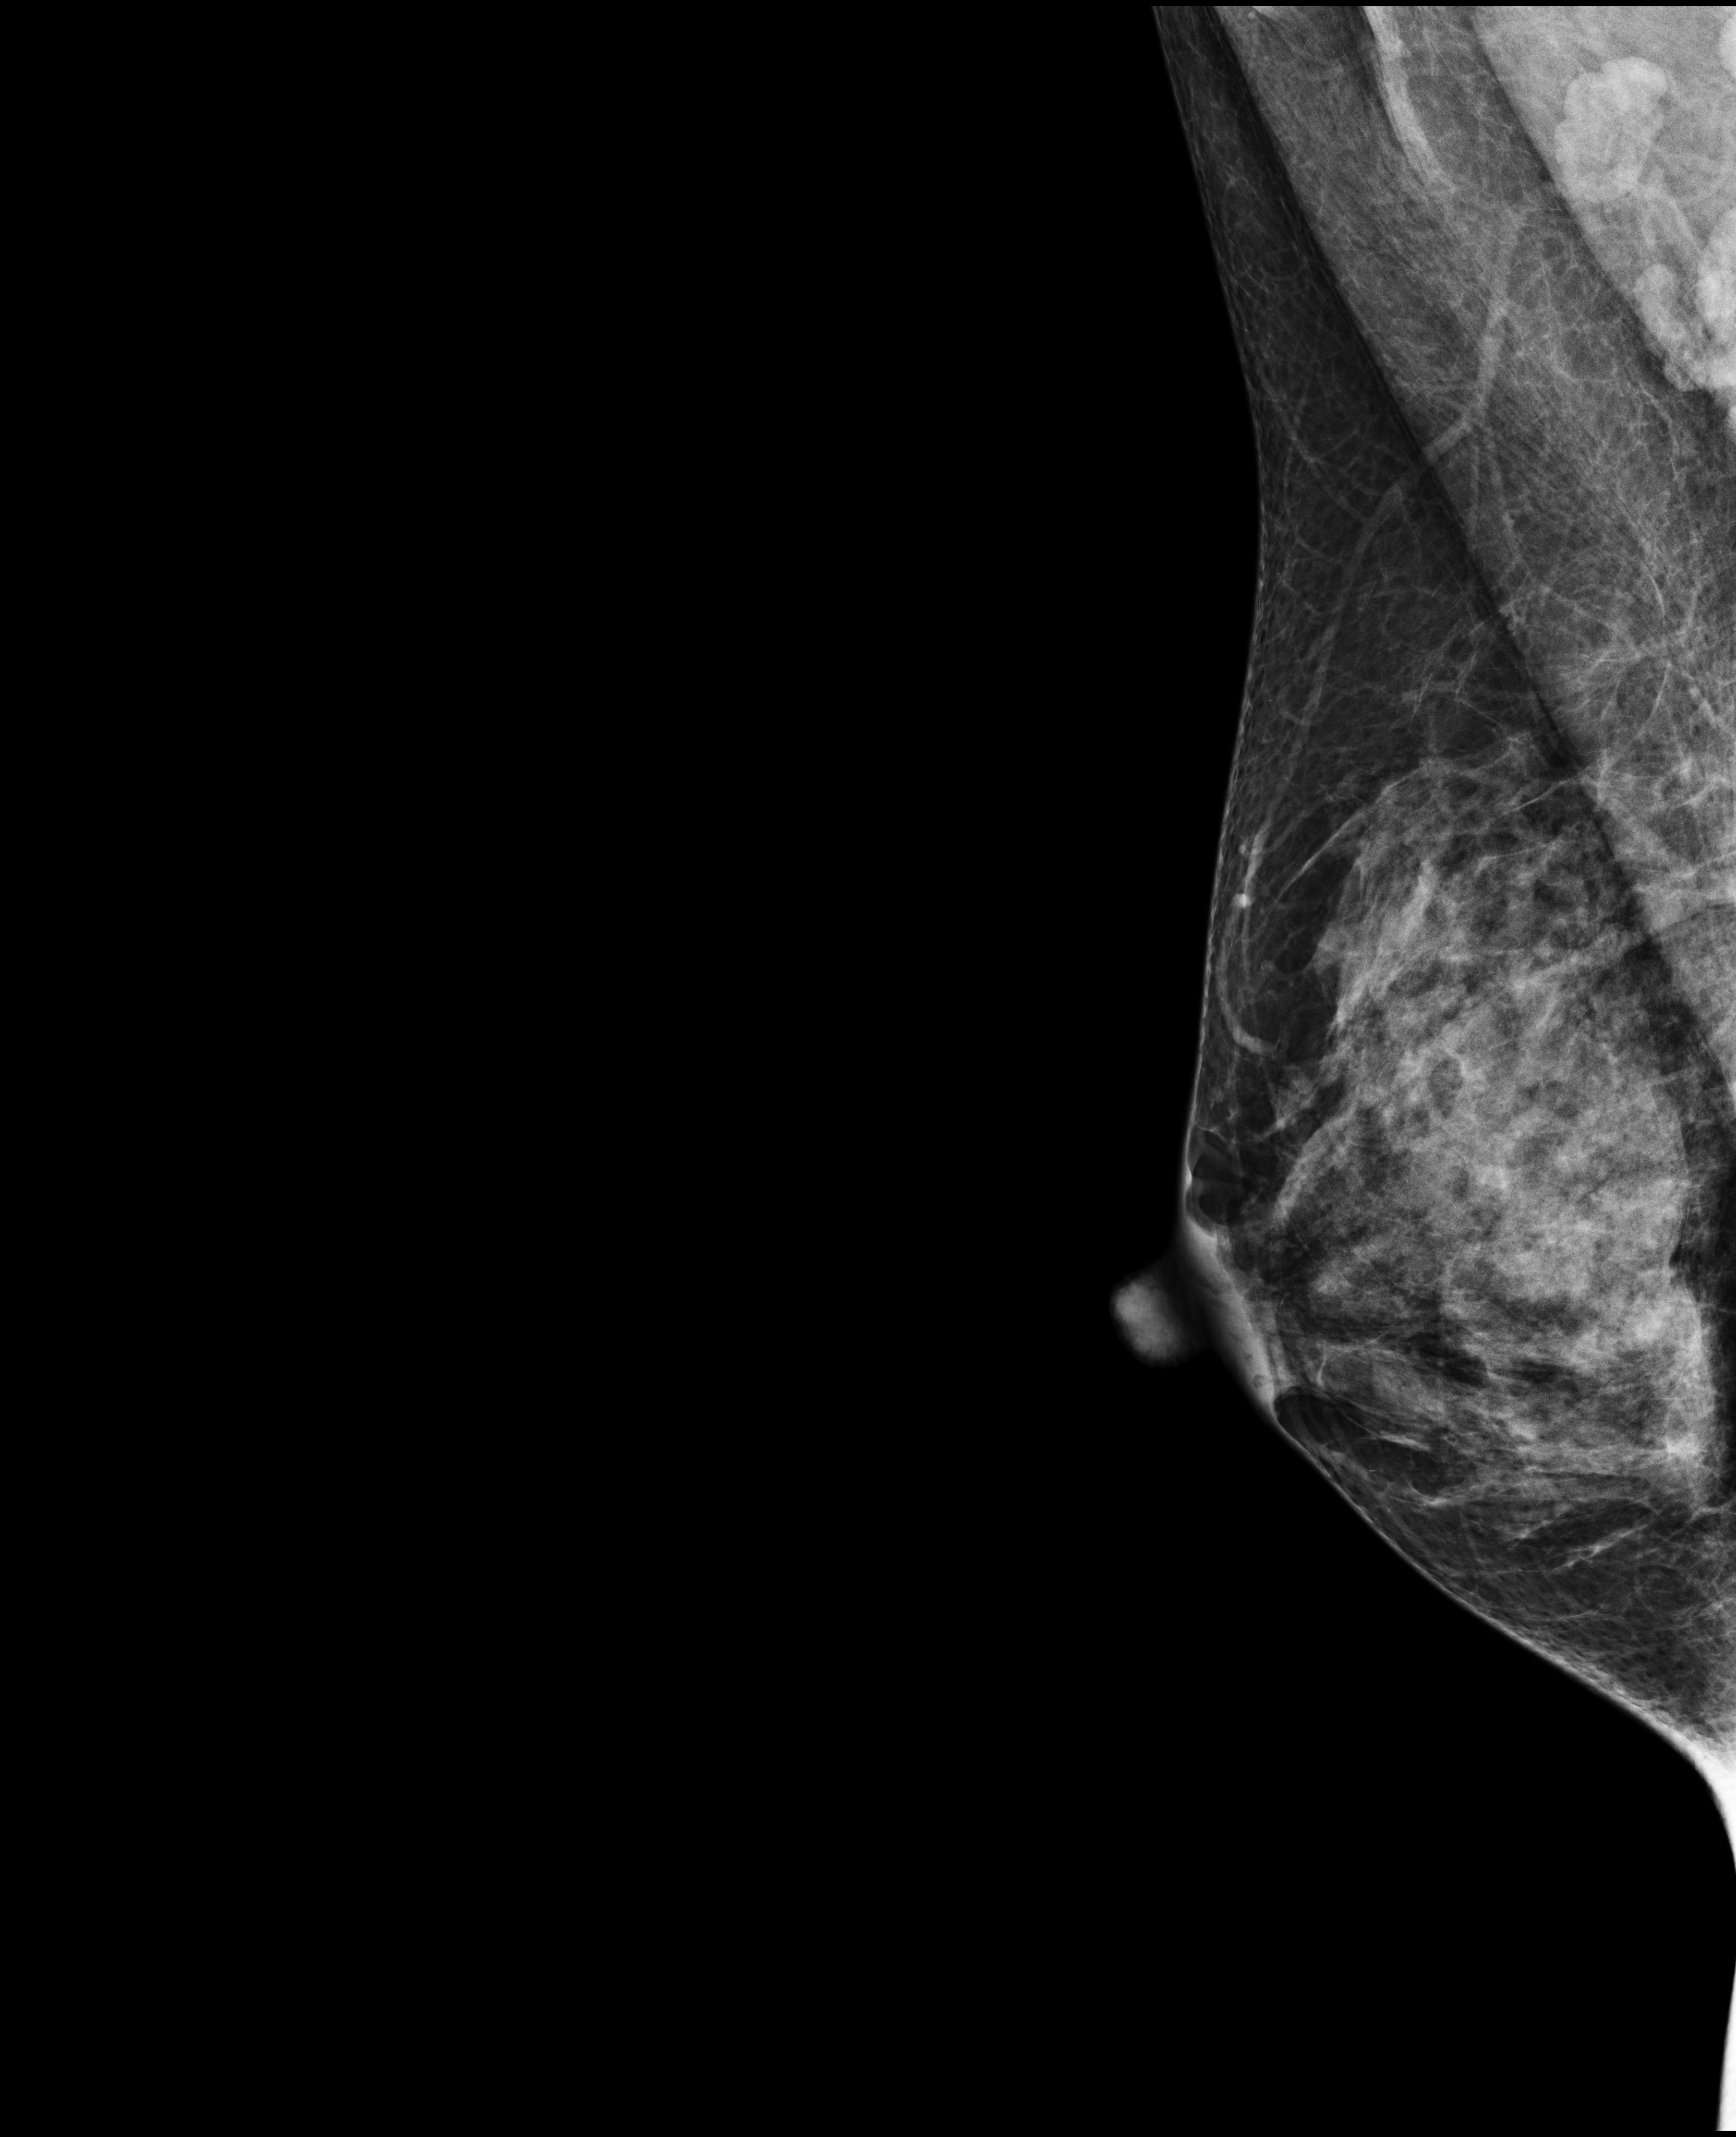
Annual screening mammography examination. Patient aged 42 years (female).
Image type: full-field digital mammogram. Breast: right. Projection: medio-lateral oblique projection.